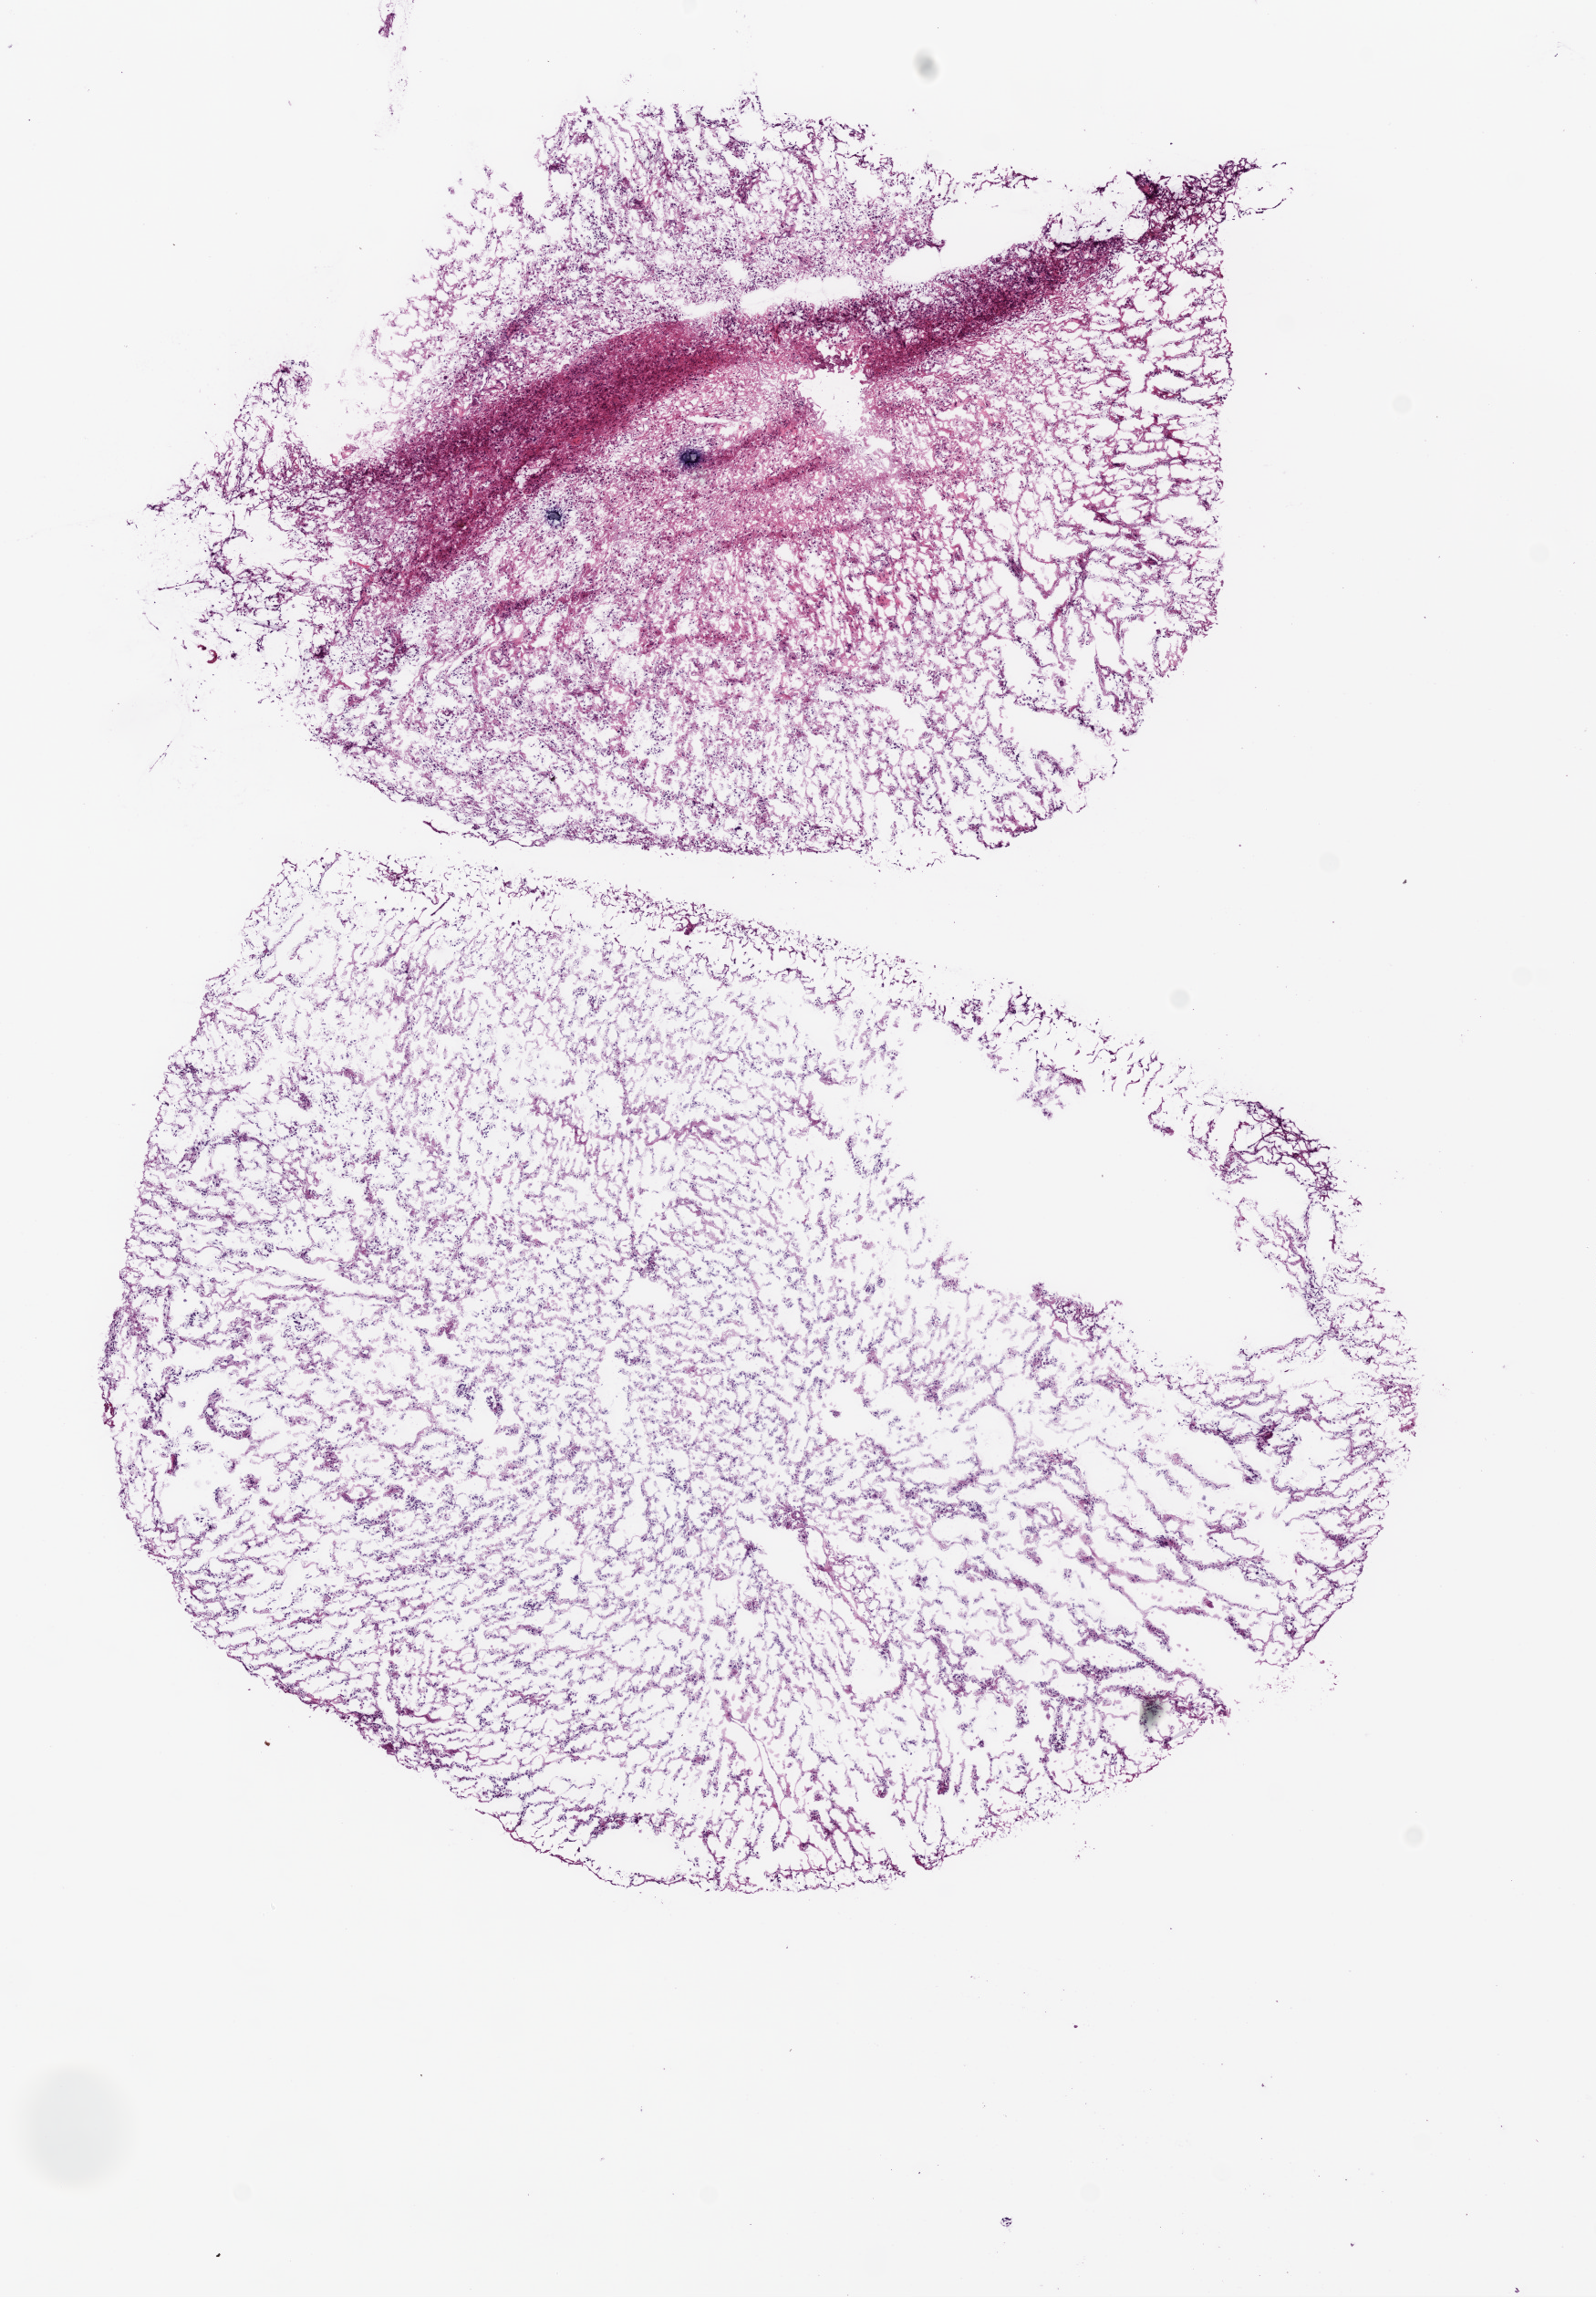
H&E-stained whole-slide image — whole scanned area (about 7.0 x 10.1 mm, from a 20x scan) shown as a low-resolution overview, frozen section, sample: primary tumour, brain. Male, age 23 years at initial diagnosis. Composition of this section per pathologist review: tumour cells 85%, tumour nuclei 80%, normal cells 10%, stromal cells 5%, necrosis 0%.
* histologic diagnosis: Glioblastoma